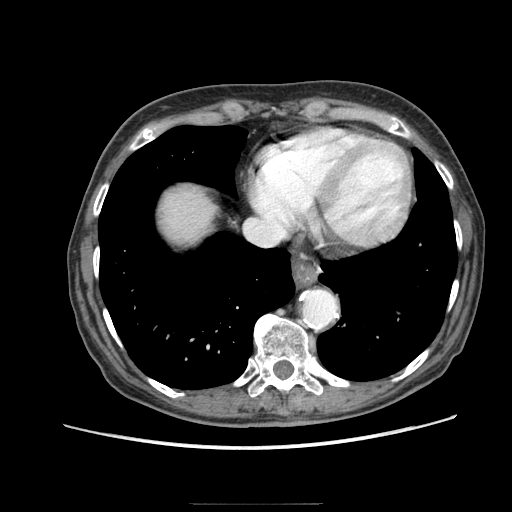
Contrast-enhanced abdominal CT (liver protocol), one axial slice. Slice 77 of 83 in the series (ordered by position). Reconstruction kernel STANDARD. 140 kVp. Soft-tissue window (W 400 / L 40 HU). 2.5 mm slice thickness. 512 × 512 image matrix, field of view 360 × 360 mm. Case-level facts recorded for this patient, not image findings: diagnosis: hepatocellular carcinoma (patient treated with transarterial chemoembolisation; whether this scan precedes or follows treatment is not stated here); TNM stage (as recorded): Stage-I; Child-Pugh class: A.
Outlined on this slice (semi-automatic segmentation, software-assisted and operator-edited):
- liver parenchyma outside the tumour (the mass and vessels are separate outlines, so this box may not span the whole liver): bounding box (x1, y1, x2, y2) in pixels: (160, 188, 214, 242)